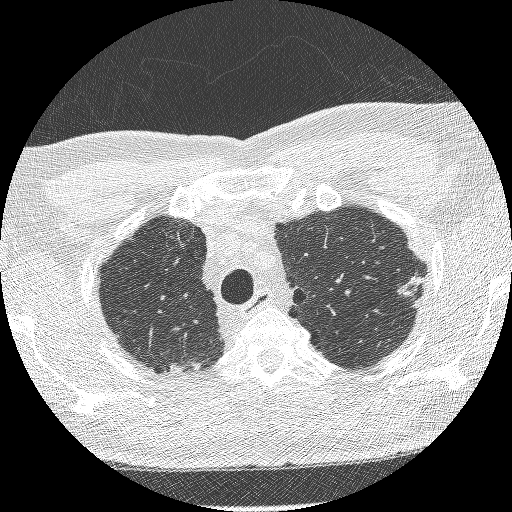
Chest CT (low-dose screening protocol), one axial image; third screening round (two years after baseline); lung window (W 1500 / L -600 HU); 1.25 mm slice thickness; lung (sharp) reconstruction kernel (BONE). Male, age 66 years at enrolment. Current smoker at enrolment.
Lesion marked by an expert reader, bounding box <391,269,435,310> (left, top, right, bottom; pixels). Reader record for this screening exam (exam-level; its link to the box is not recorded): non-calcified nodule or mass ≥4 mm, left lower lobe, 15 × 9 mm, spiculated (stellate) margins, soft tissue attenuation, pre-existing on the prior screen: yes; interval growth: yes. Official screen result: positive, other.